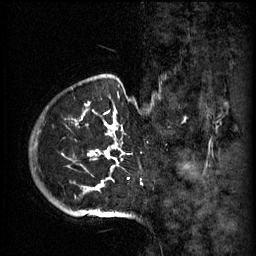
Breast MRI (dynamic contrast-enhanced), one sagittal slice. Slice 51 of 60 in the series (ordered by position). 3 images stored at this slice position (order not interpretable as contrast timing). 1.5 T. TE 4.2 ms, TR 11 ms. 256 × 256 image matrix, field of view 200 × 200 mm. Female patient, age 51 years.
Outlined on this slice (semi-automatically segmented with operator editing):
- analysis volume of interest (the breast-tissue region the enhancement analysis was run in; not a lesion): bounding box <48,82,159,197> (left, top, right, bottom; pixels)
- tumour enhancement mask (voxels above the 70 % enhancement threshold inside the analysis volume of interest): <89,114,129,187>